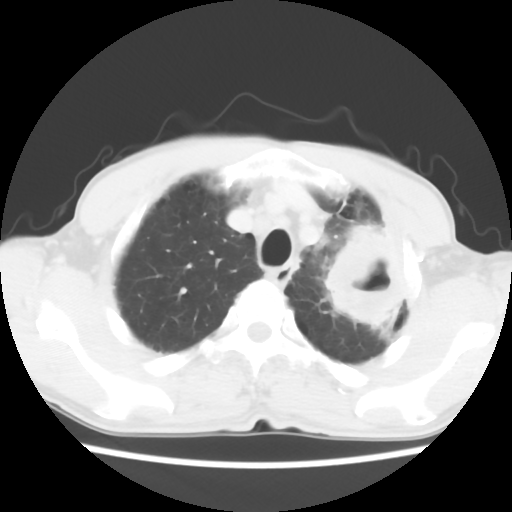
Chest CT, one axial slice; slice 49 of 60 in the series (ordered by position); reconstruction kernel STANDARD; 120 kVp; lung window (W 1500 / L -600 HU); 512 × 512 image matrix. Patient: male, 64 years. Case-level facts recorded for this patient, not image findings: clinical TNM (as recorded): T3 N3 M0; histopathological grade: G3.
Annotated regions visible in this slice (rectangle marked by the reading radiologist):
- lung tumour (recorded histology: adenocarcinoma): box from (x=316, y=209) to (x=412, y=339) px